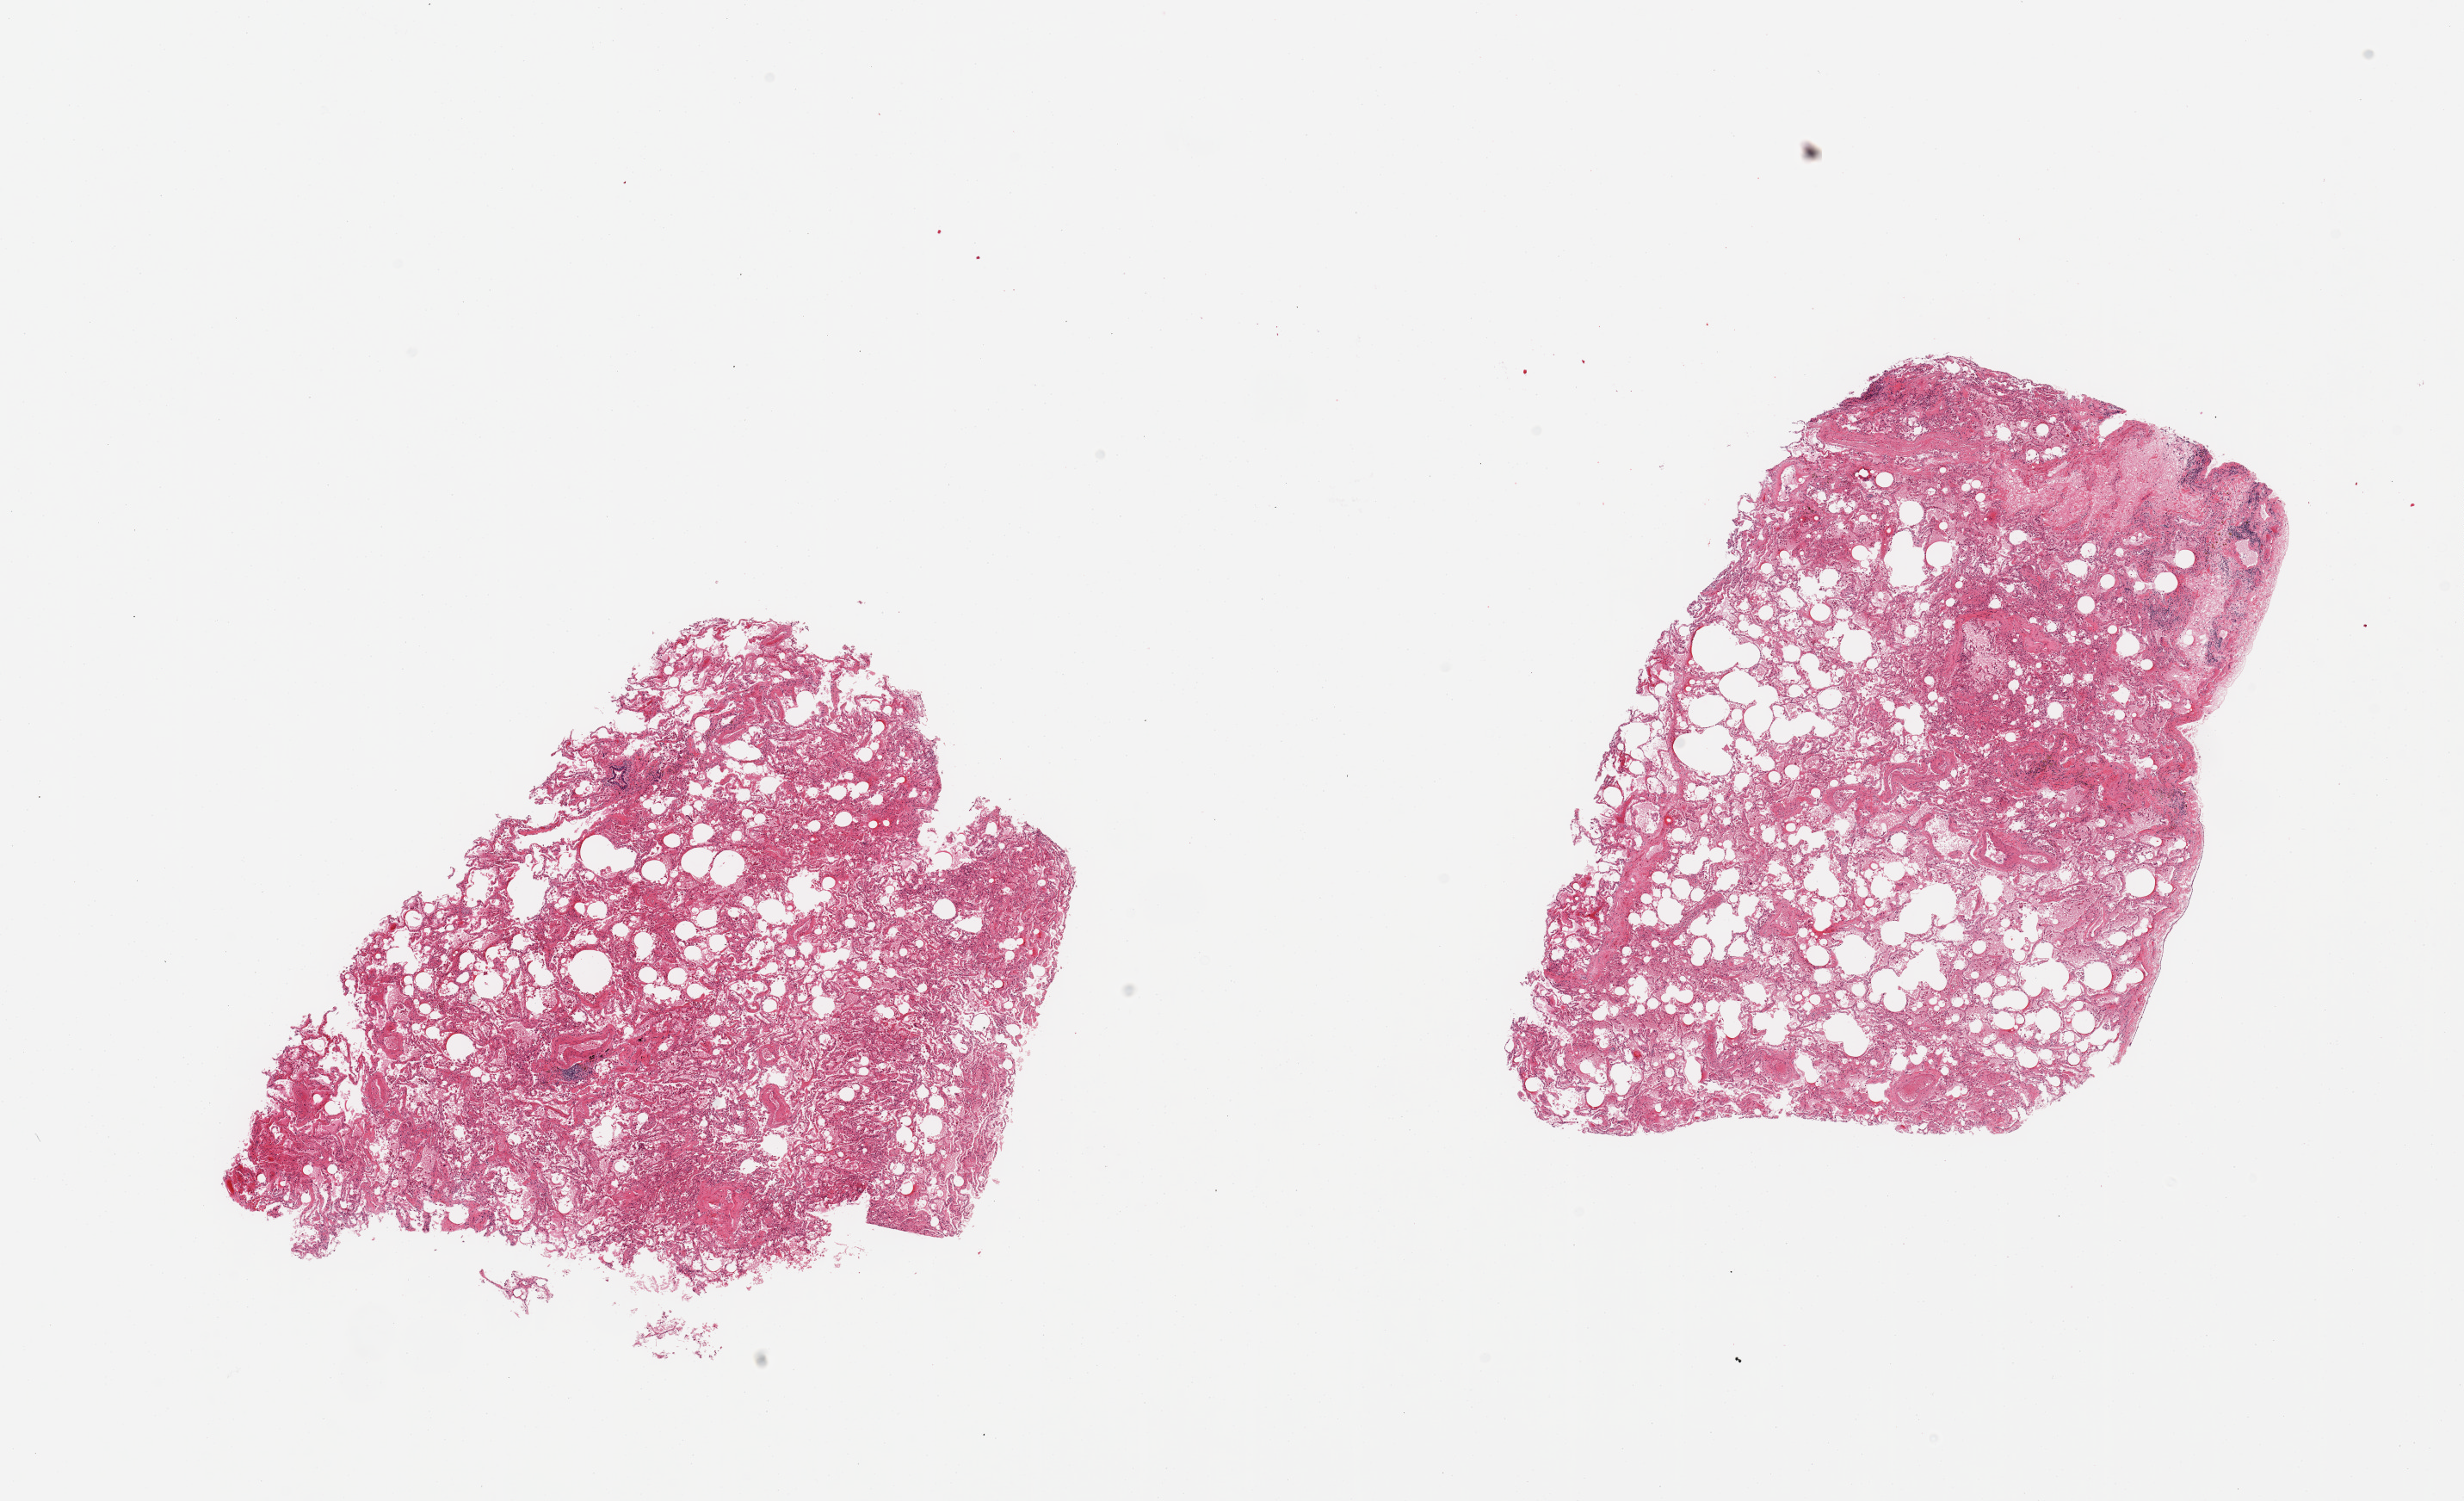
Haematoxylin and eosin whole-slide image — whole scanned area (about 22.6 x 13.8 mm) shown as a low-resolution overview; PAXgene-fixed paraffin-embedded (PFPE) section; section of lung (target tissue); tissue donor sample. Donor: male.
Pathologist's review note for this sample: 2 pieces; patchy emphysema, alveolar edema & hemorrhage; partial inclusion of pleura.